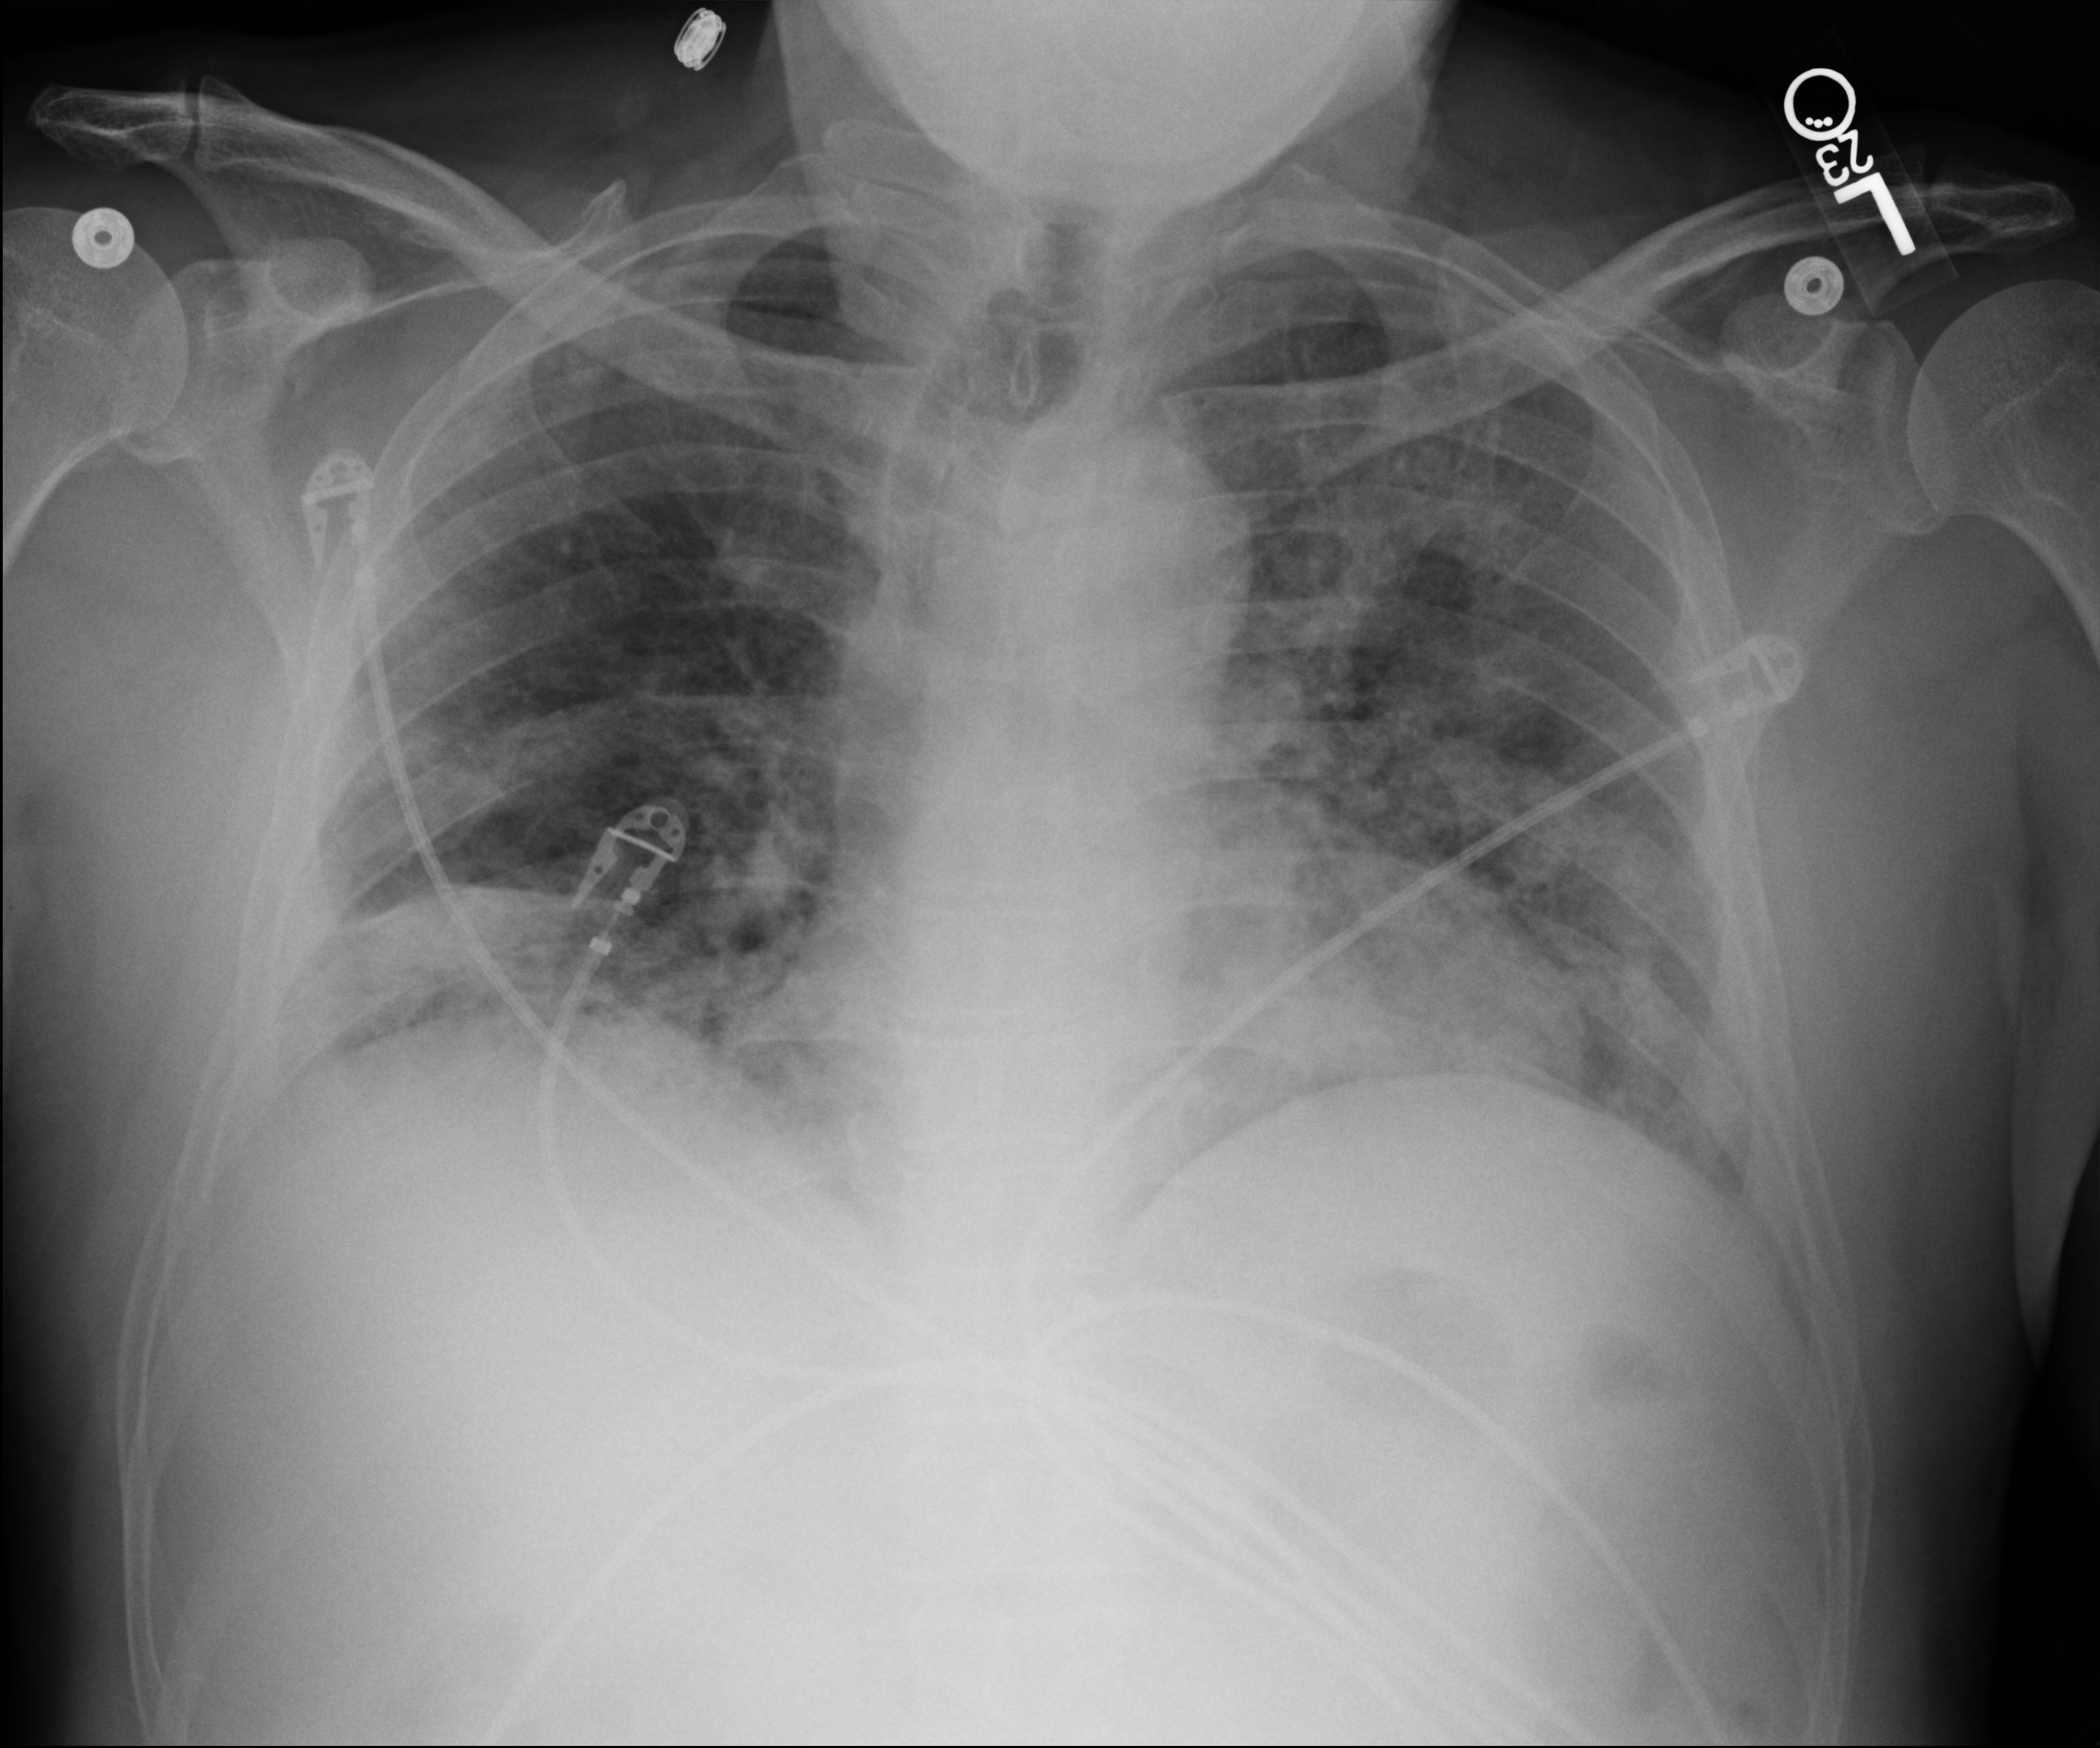
Bedside chest radiograph (computed radiography); anteroposterior (AP) projection. Male patient hospitalised with COVID-19, age 18–59 years.
Admission-level facts for this patient (not findings on this image; timing relative to this image not recorded): admitted to intensive care during this hospital stay: no; length of hospital stay: 29 days; COPD (admission record): no.